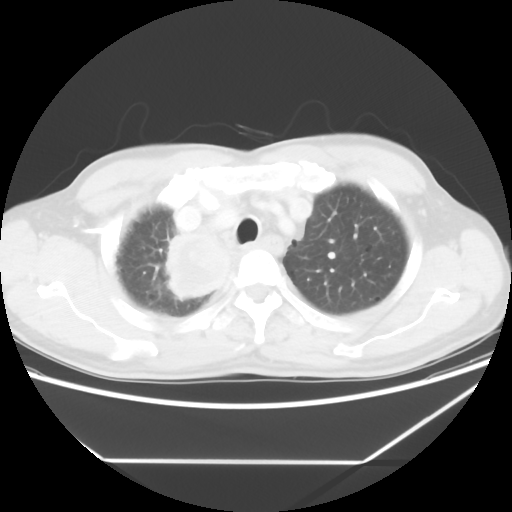
Chest CT, one axial slice. Position 50 of 60 along the scan axis. Reconstruction kernel STANDARD. 120 kVp. Lung window (W 1500 / L -600 HU). 5 mm slice thickness. 512 × 512 image matrix, field of view 367 × 367 mm. Male patient, age 58 years. From the clinical record (not read from this slice): clinical TNM (as recorded): T2 N2 M0.
Structures marked on this image (bounding box drawn by a radiologist):
- lung tumour (recorded histology: squamous cell carcinoma): bounding box (x1, y1, x2, y2) in pixels: (163, 230, 237, 309)